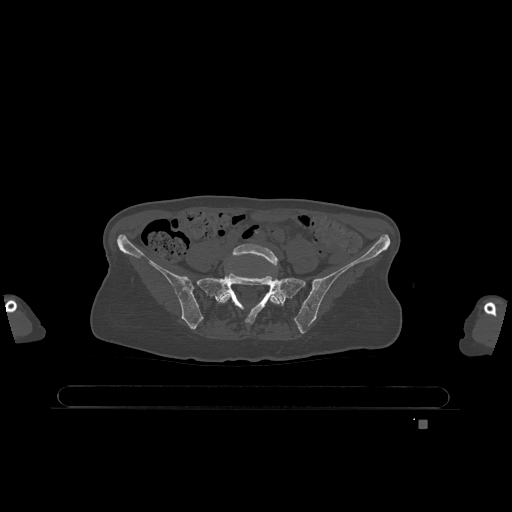
CT including the spine, one axial slice. Slice 209 of 1317 in the series (ordered by position). Bone window (W 1800 / L 400 HU). 512 × 512 image matrix, field of view 500 × 500 mm. Female patient, age 74 years. Case-level facts recorded for this patient, not image findings: primary cancer: lung; vertebrae with lytic lesions (as recorded): T1, T4, T5, T6, L4, L5.
Annotated regions visible in this slice (semi-automatic segmentation, software-assisted and operator-edited):
- L5 vertebra: bounding box (x1, y1, x2, y2) in pixels: (219, 244, 283, 306)